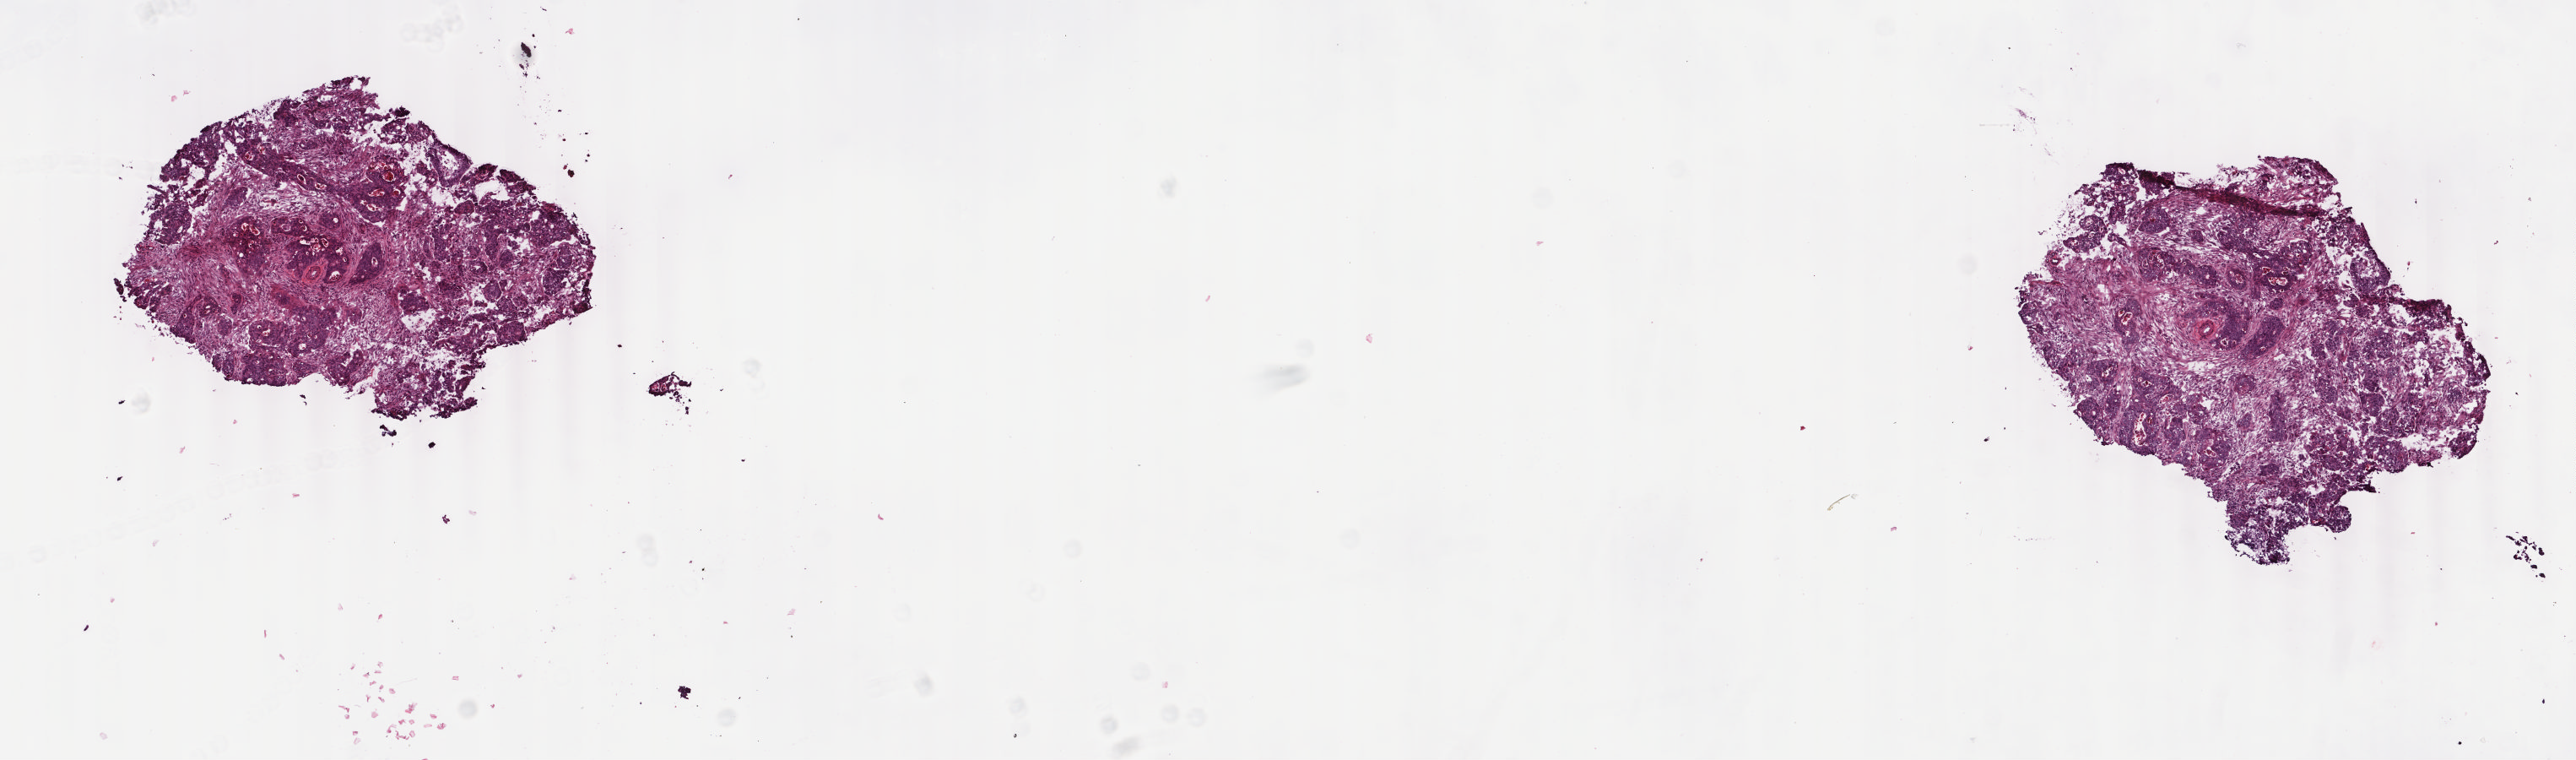
Digitized H&E-stained tissue section (whole slide) — a low-resolution overview of the entire scanned area, about 12.1 x 3.6 mm (slide scanned at 40x); frozen section; sample: primary tumour, rectum. Patient: male, age at initial diagnosis 86 years. Composition of this section per pathologist review: tumour cells 80%, tumour nuclei 80%, normal cells 0%, stromal cells 15%, necrosis 5%. Inflammatory infiltration, as recorded: lymphocyte infiltration 3%, monocyte infiltration 1%, neutrophil infiltration 1%.
TNM: T2 N0 M0. Histologic diagnosis: Adenocarcinoma, NOS. AJCC pathologic stage: I (6th edition).